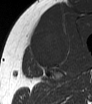
MRI of an extremity soft-tissue mass, one axial slice; position 39 of 62 along the scan axis; MR volume resampled by the dataset authors to the PET/CT grid (not the native acquisition matrix); 92 × 104 image matrix, field of view 90 × 102 mm. Male patient. From the clinical record (not read from this slice): histological type: mixoid liposarcoma; grade: low; site of the primary tumour: left thigh.
Annotated regions visible in this slice (expert contour drawn on MRI and transferred to this co-registered scan by the dataset authors):
- gross tumour volume (mass): bounding box (x1, y1, x2, y2) in pixels: (28, 28, 68, 68)